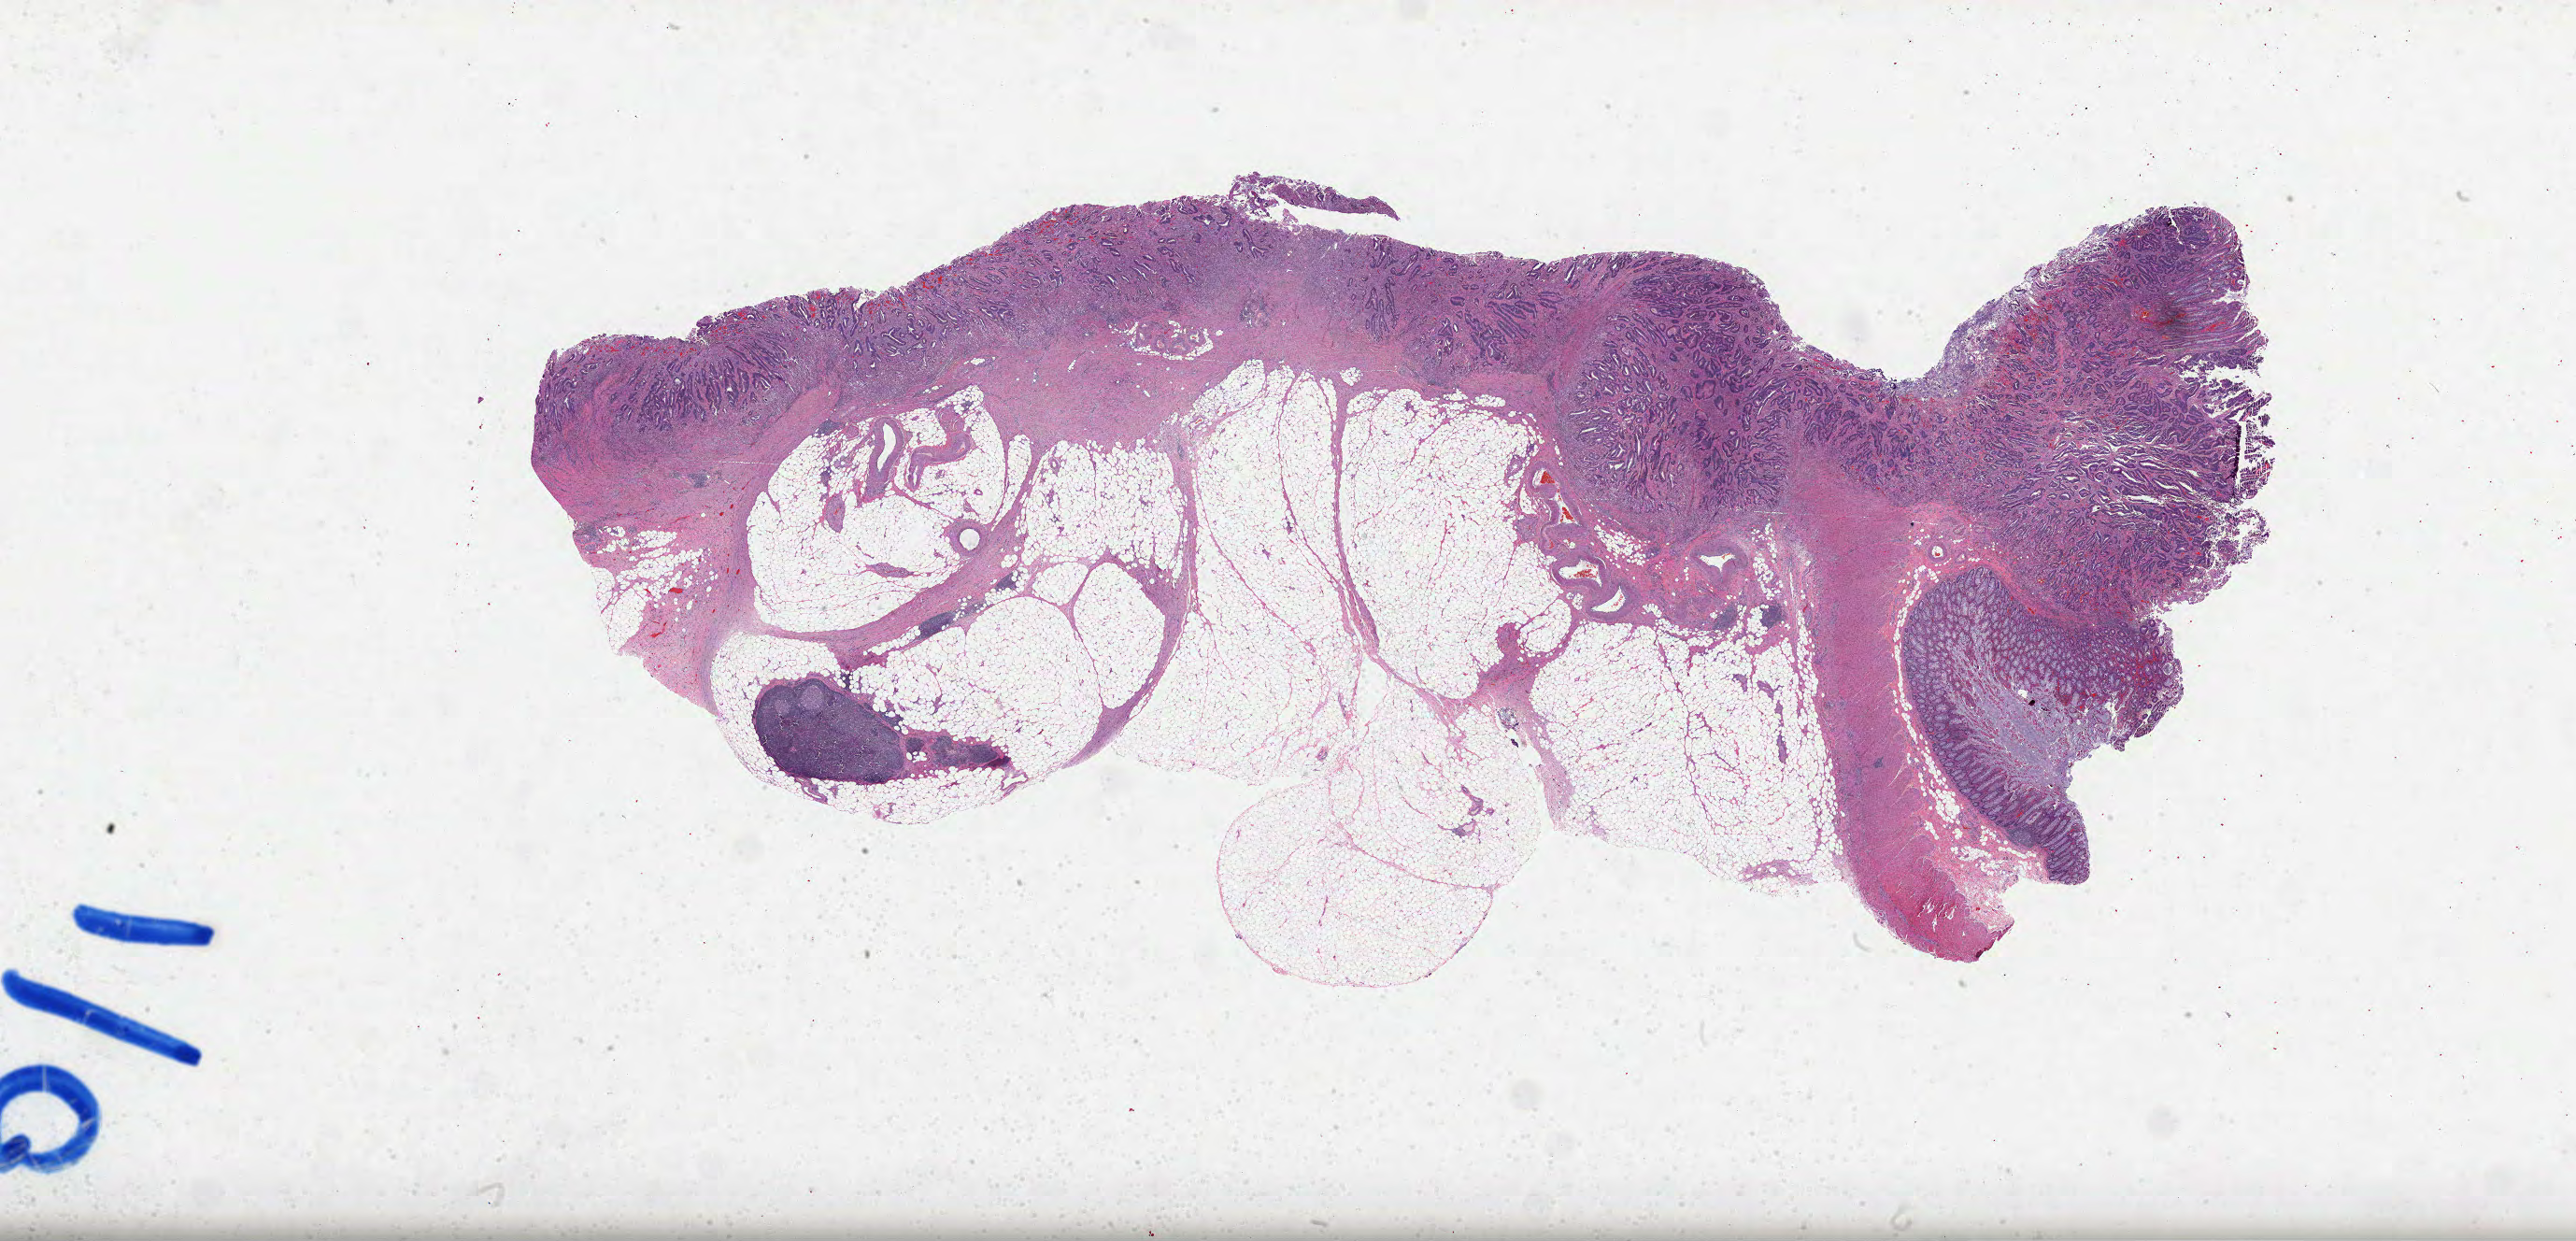
H&E whole-slide image, shown as a low-resolution overview of the whole scanned area (about 44.5 x 21.4 mm), formalin-fixed paraffin-embedded (FFPE) diagnostic section, colon, primary tumour sample. Male, age 44 years at initial diagnosis.
* AJCC pathologic stage: IIA (7th edition)
* lymph nodes positive (case pathology): 0 of 44 examined
* diagnosis: Adenocarcinoma, NOS (ascending colon)